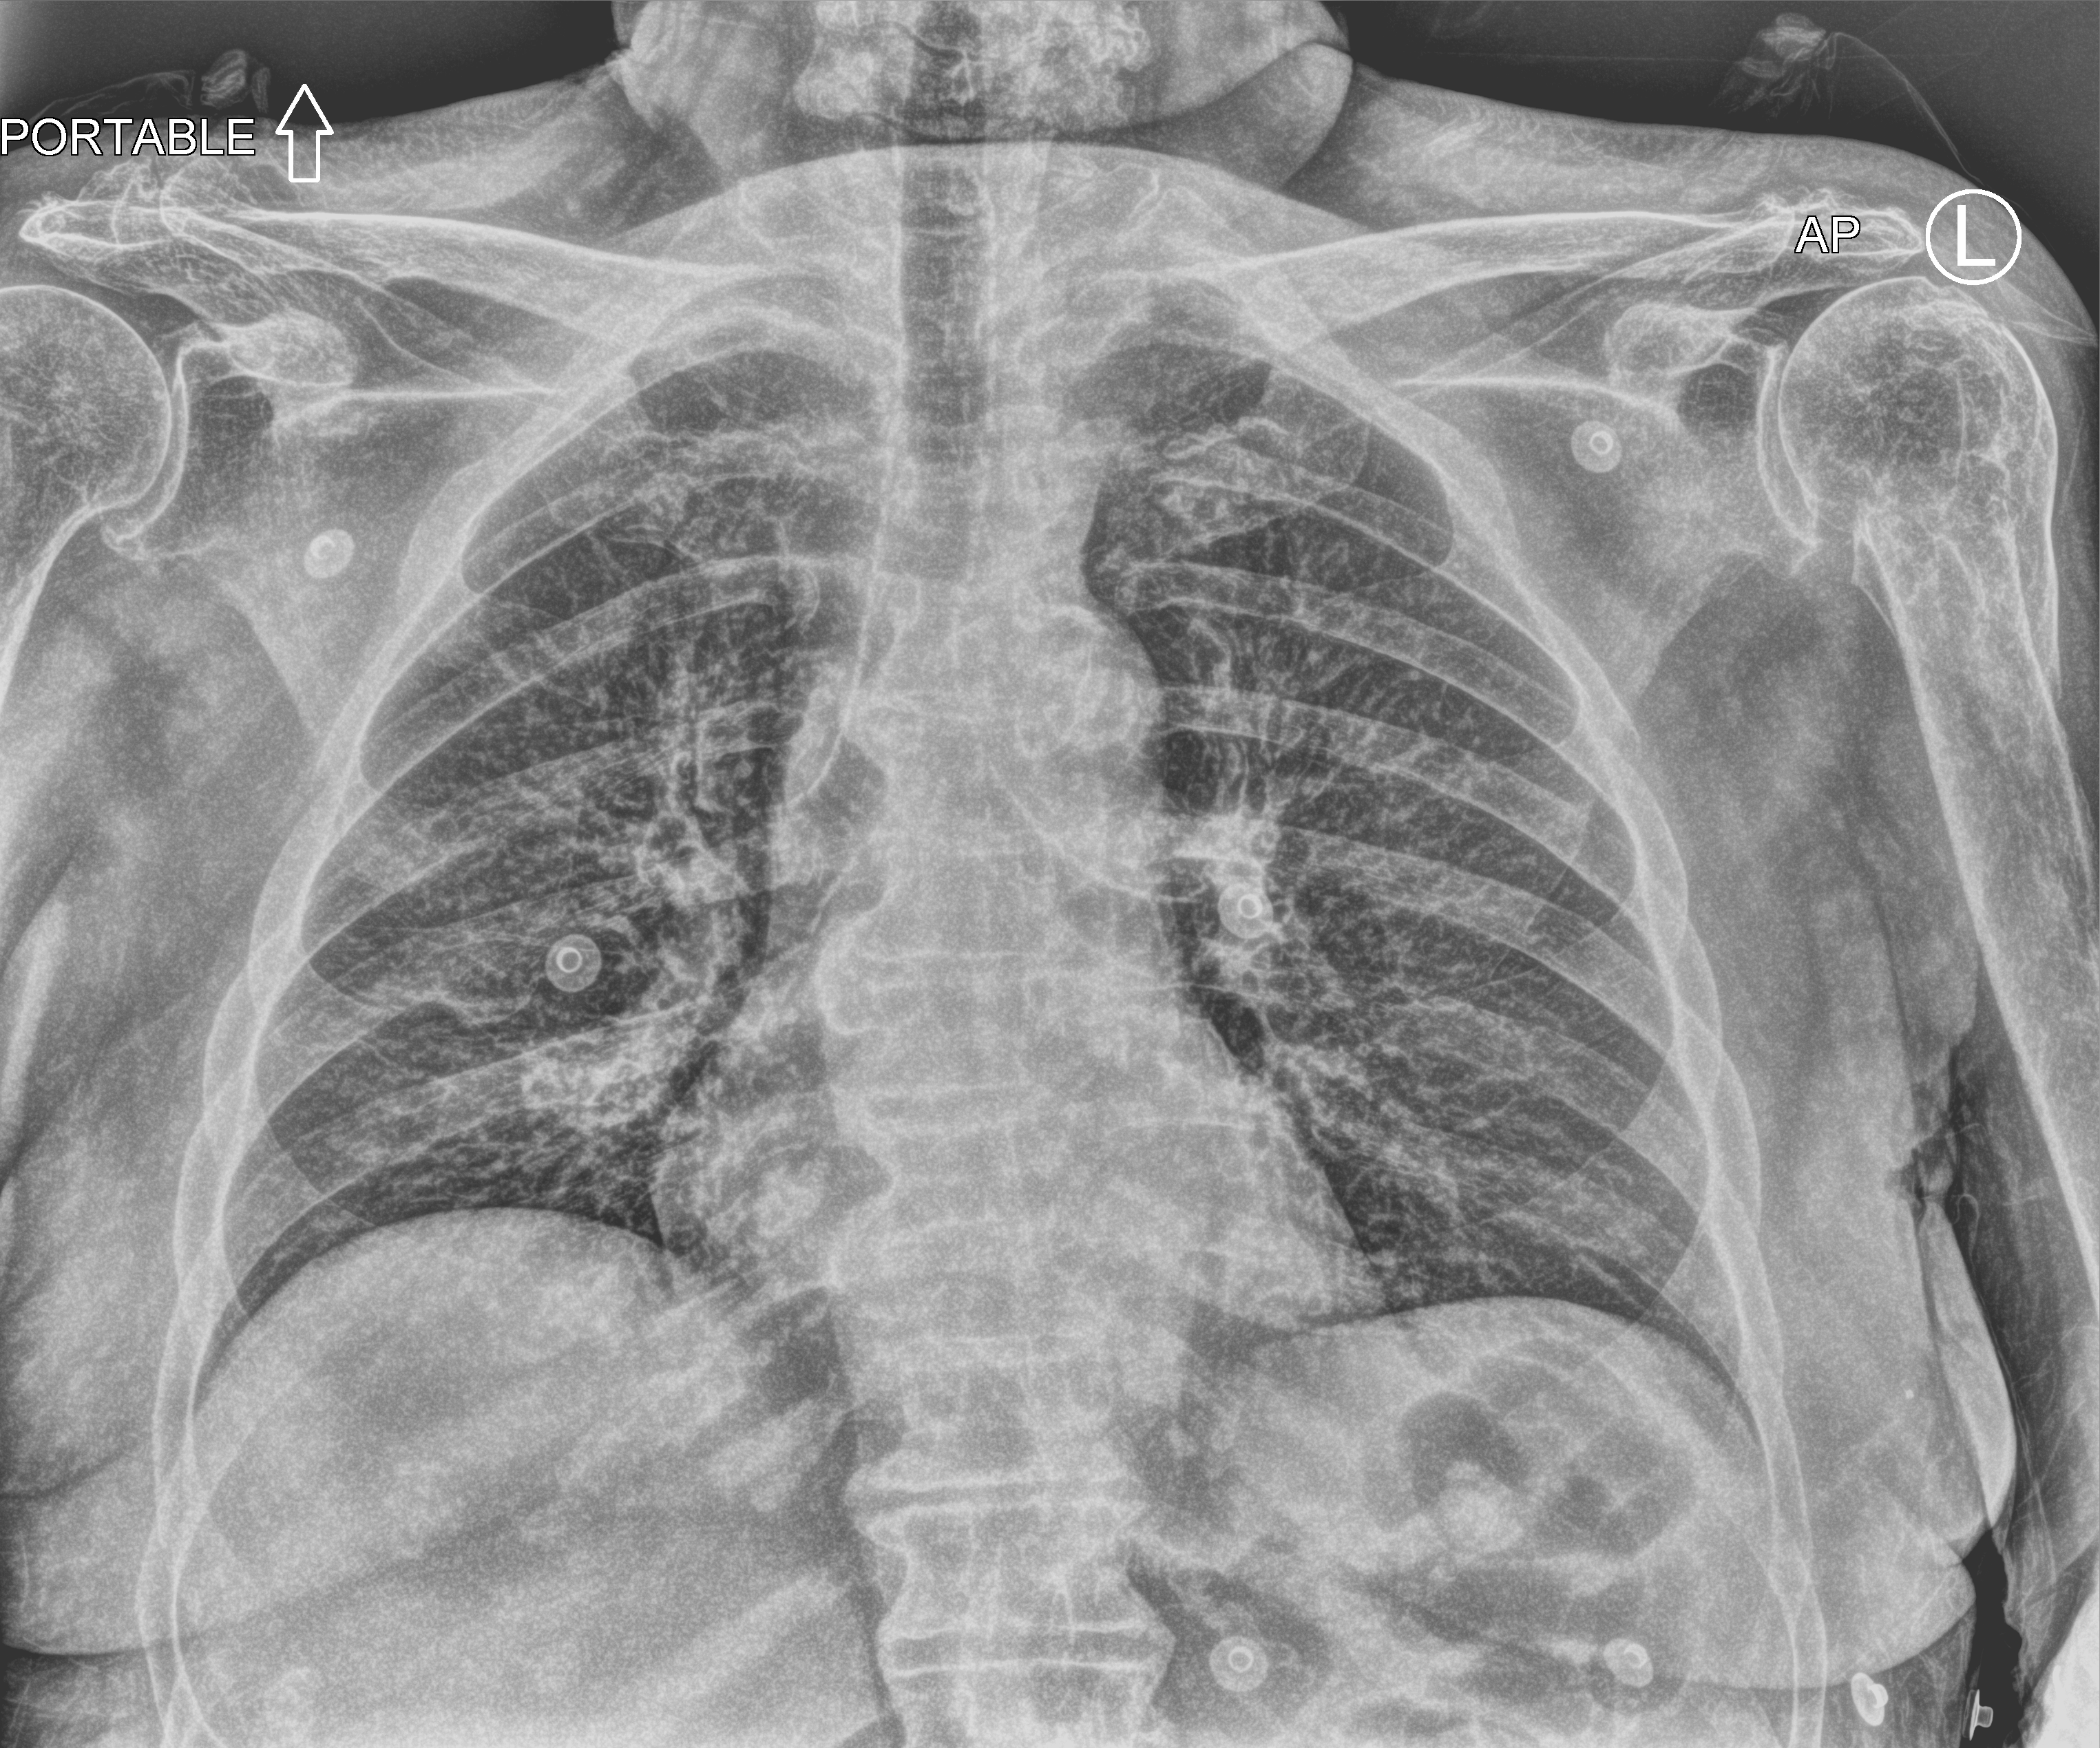
Portable chest radiograph; anteroposterior (AP) projection. Female patient hospitalised with COVID-19, age 75–90 years.
Hospital-stay facts (about this admission, not read from this image; timing relative to this image not recorded): chronic kidney disease (admission record): yes; diabetes (admission record): yes.